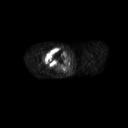
FDG PET of an extremity soft-tissue mass (from a PET/CT study), one axial slice; slice 254 of 311 in the series (ordered by position); 3.27 mm slice thickness; 128 × 128 image matrix. Patient: male, 50 years. From the clinical record (not read from this slice): histological type: undifferentiated - pleiomorphic; grade: high; site of the primary tumour: right thigh.
Outlined on this slice (expert contour drawn on MRI and transferred to this co-registered scan by the dataset authors):
- gross tumour volume including surrounding oedema: bounding box [x1, y1, x2, y2] px = [42, 48, 66, 67]
- gross tumour volume (mass): [45, 49, 65, 66]